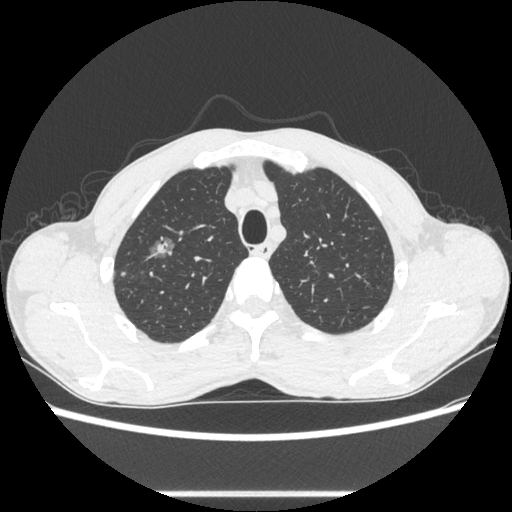
Chest CT, one axial slice. Position 486 of 600 along the scan axis. Lung window (W 1500 / L -600 HU). 0.62 mm slice thickness. 512 × 512 image matrix. Male patient, age 54 years. Case-level facts recorded for this patient, not image findings: clinical TNM (as recorded): T1a N0 M0.
Structures marked on this image (rectangle marked by the reading radiologist):
- lung tumour (recorded histology: adenocarcinoma): bounding box (x1, y1, x2, y2) in pixels: (142, 227, 177, 263)